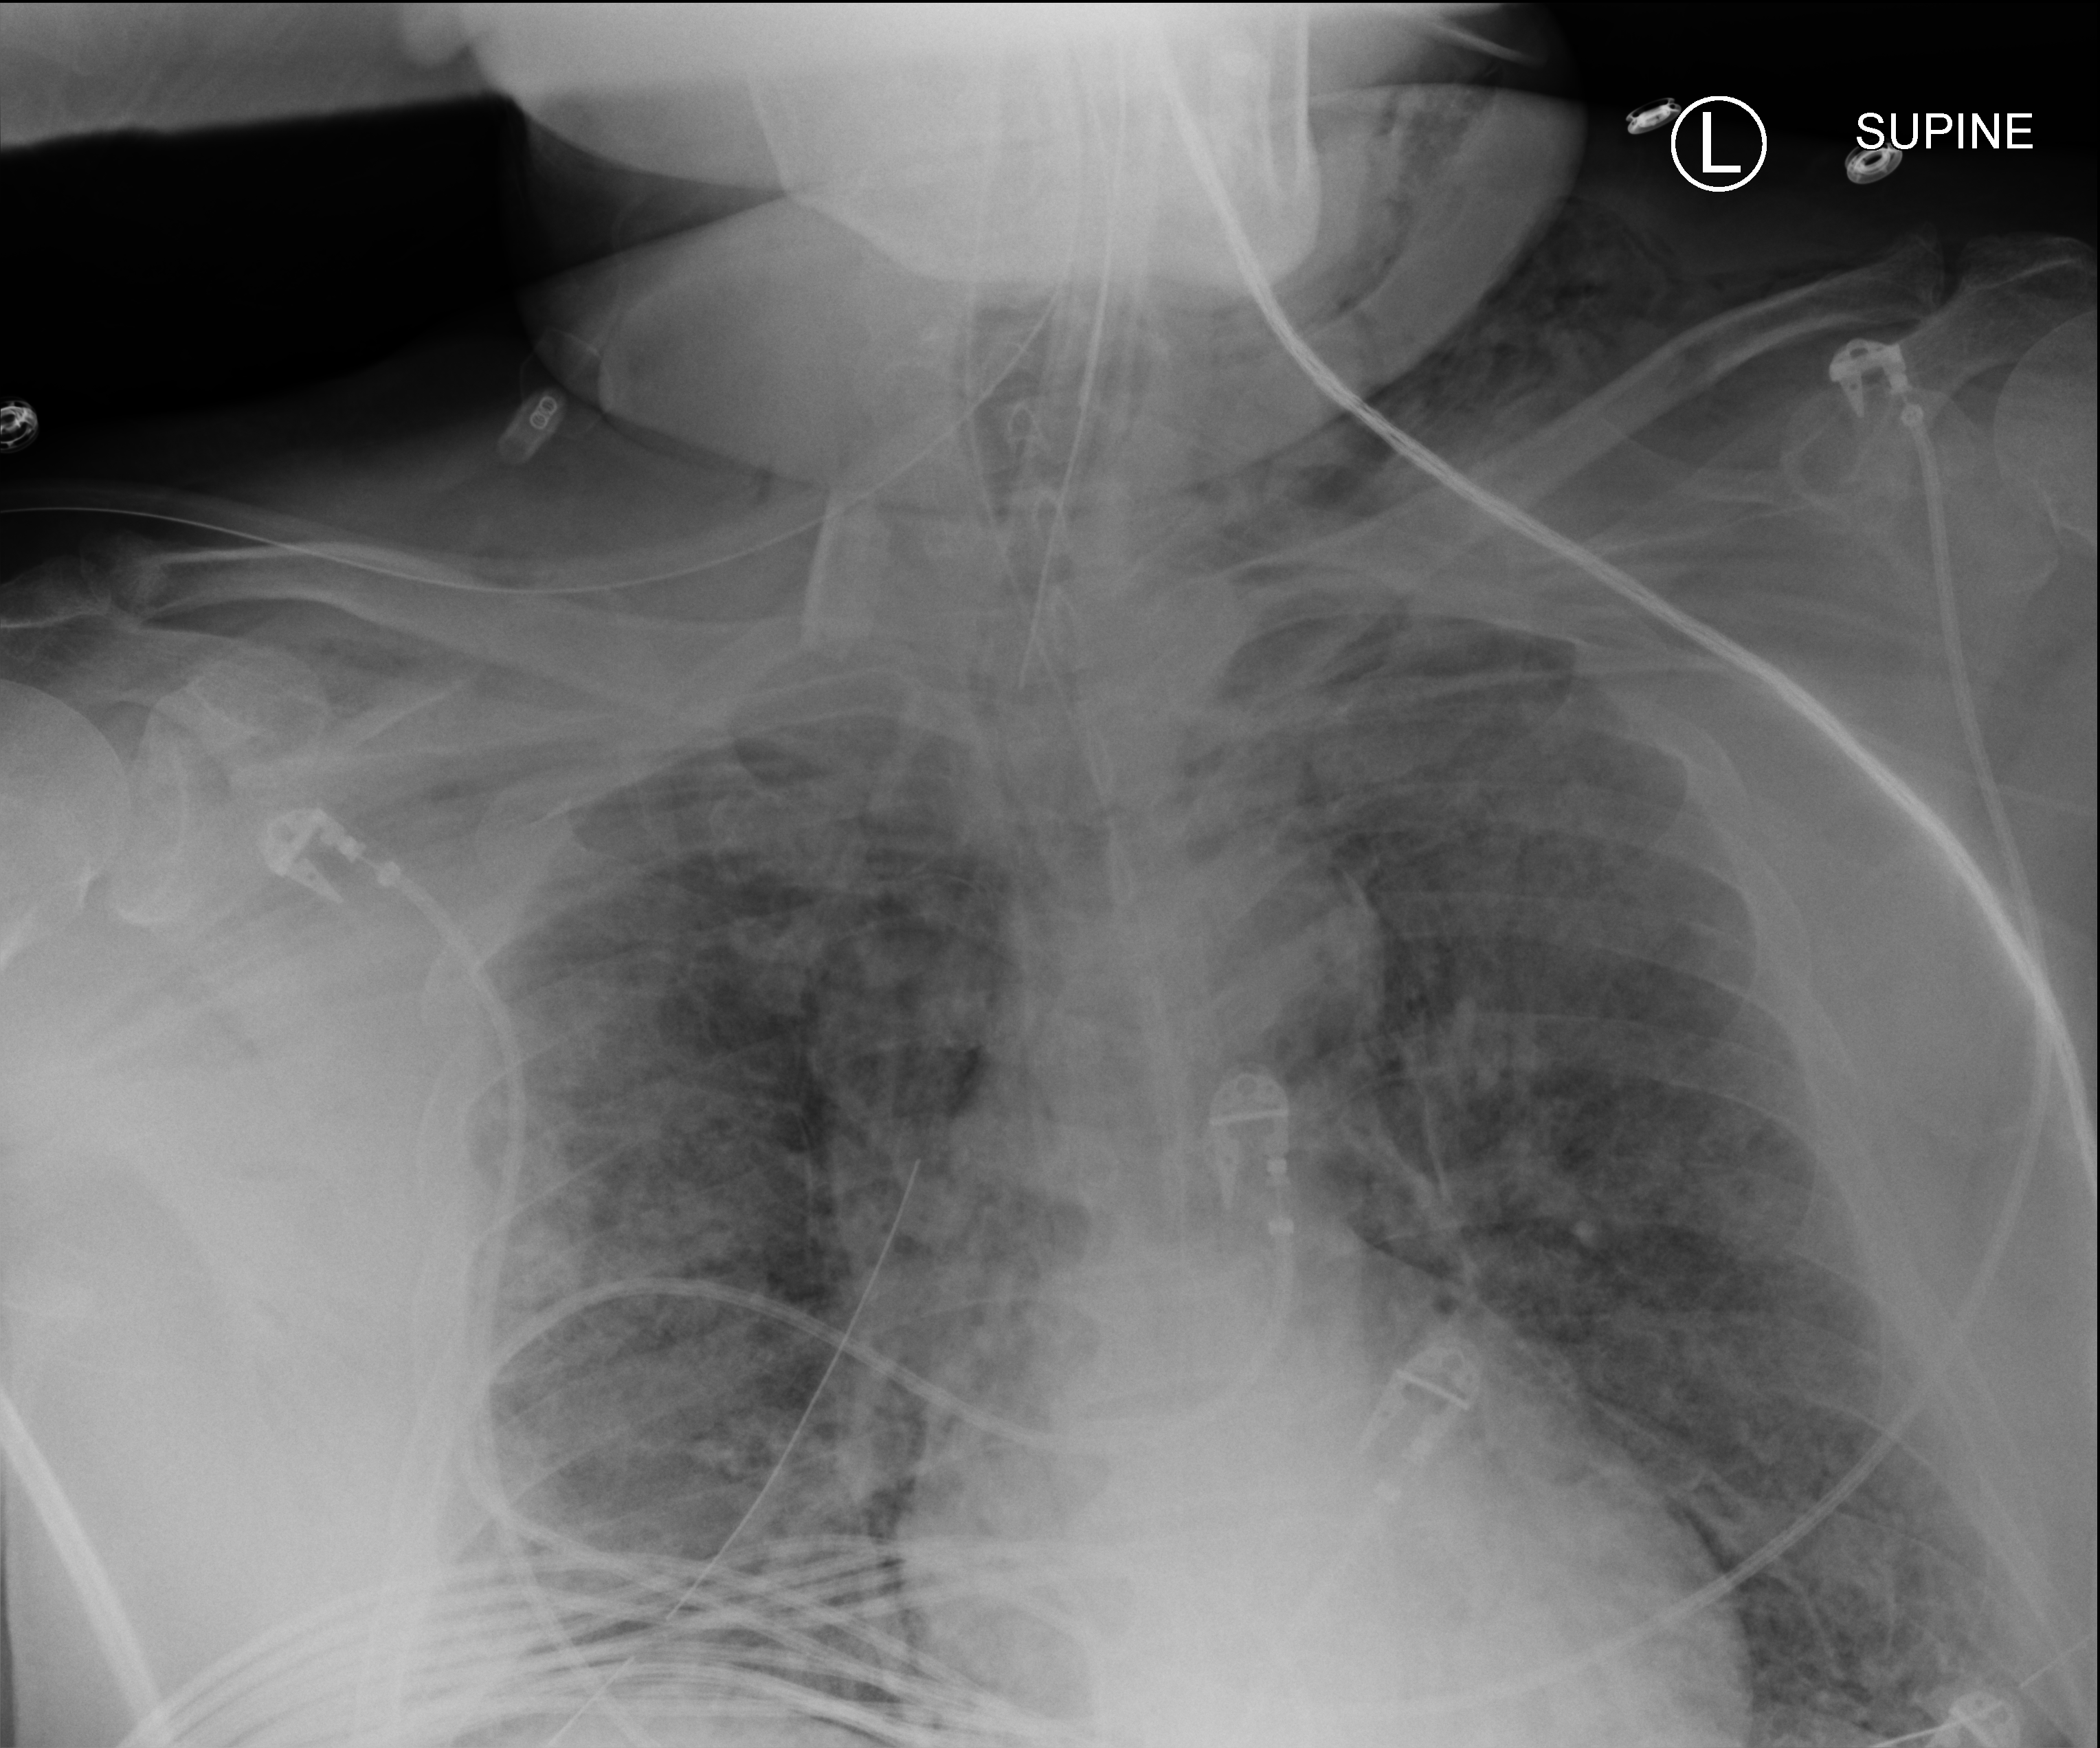
Chest X-ray (portable). Adult patient hospitalised with COVID-19, age 18–59 years.
From the hospital-stay record, not from the radiograph (when in the stay this image was taken is not recorded): other chronic lung disease (admission record): no; mechanically ventilated during this hospital stay: yes; admitted to intensive care during this hospital stay: yes.